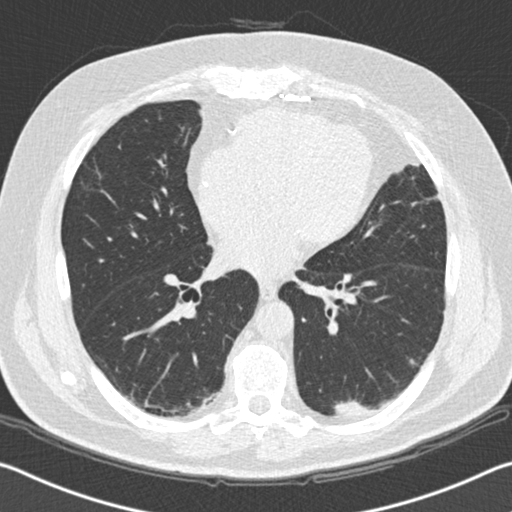
Axial slice from a low-dose chest CT screening exam, second annual screen, lung window (W 1500 / L -600 HU), standard (soft-tissue) reconstruction kernel (B30f), slice 92 of 172 in the series, 512 × 512 image matrix, field of view 340 × 340 mm. Male, age 65 years at enrolment.
• Expert-annotated lung lesion, bounding box <325,389,390,435> (left, top, right, bottom; pixels).
• The exam's reader record, not a measurement of the box and not confirmed to be the same lesion: non-calcified nodule or mass ≥4 mm, left lower lobe, 19 × 11 mm, spiculated (stellate) margins, soft tissue attenuation, pre-existing on the prior screen: yes; interval growth: yes.
• Participant outcome: lung cancer diagnosed 179 days after this screen — squamous cell carcinoma, NOS, left lower lobe, moderately differentiated (G2), stage IA (AJCC 6th edition), 20 mm at pathology.